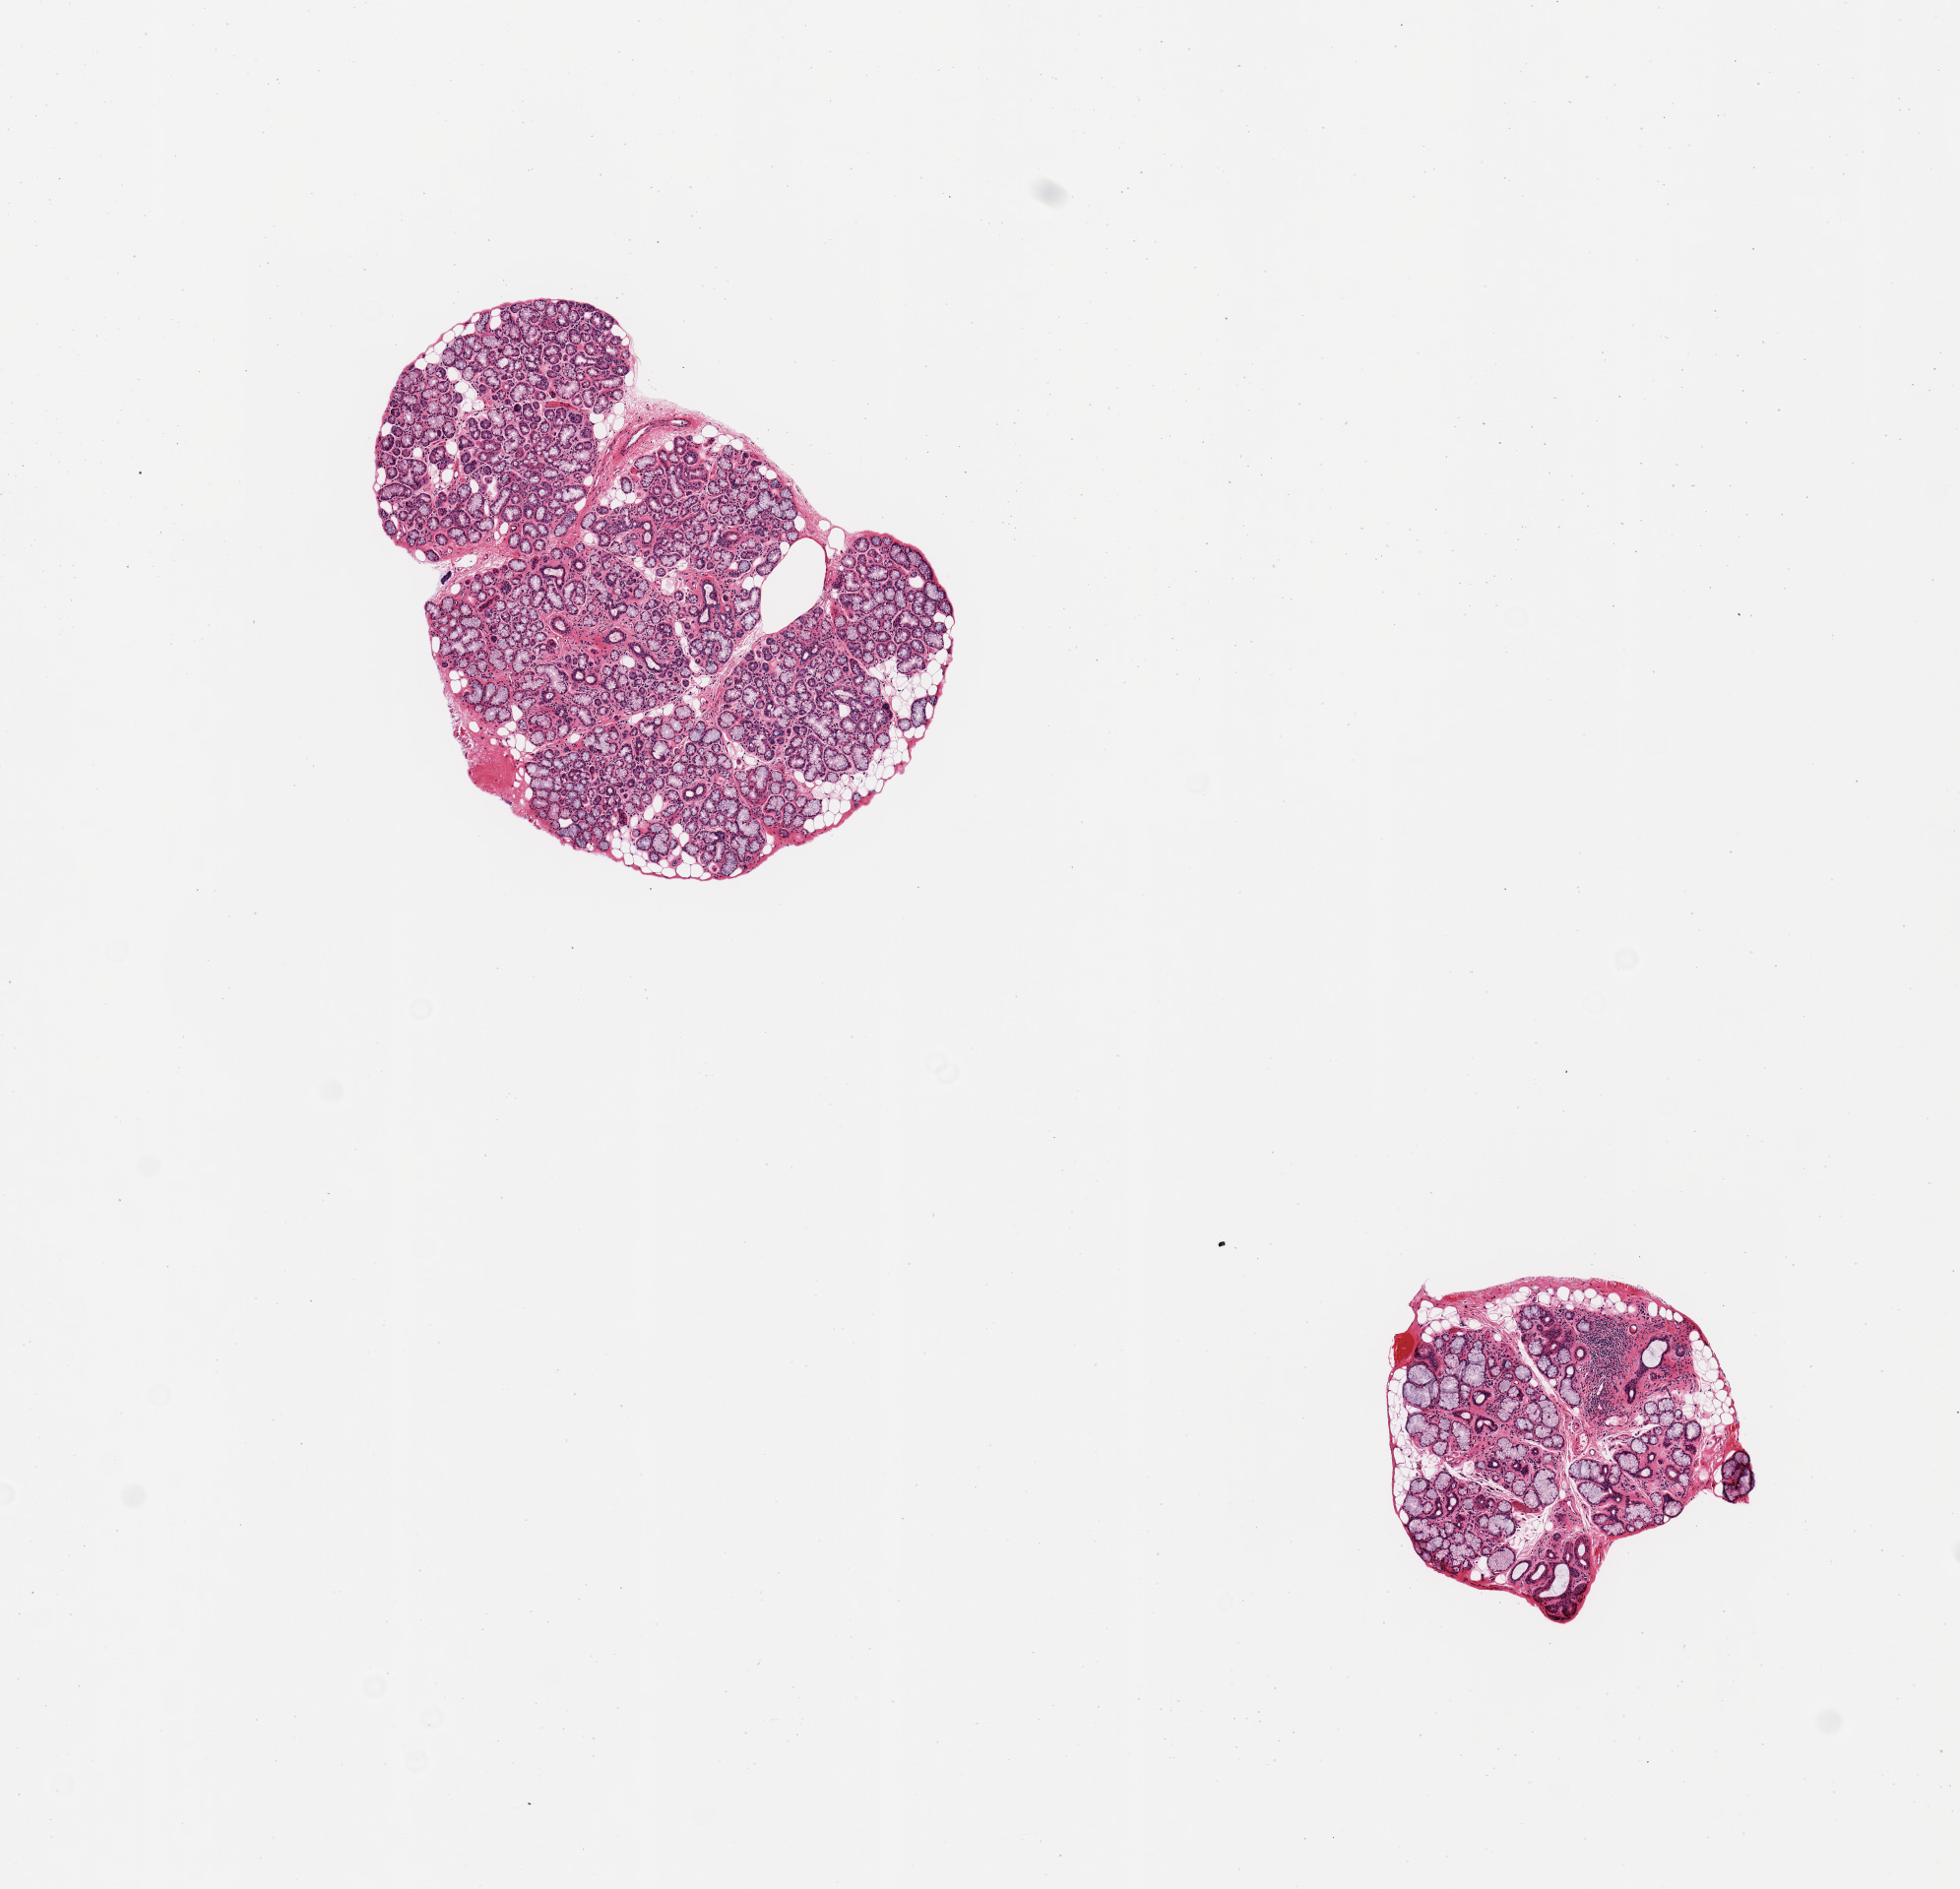
Digitized haematoxylin and eosin-stained section — shown as a low-resolution overview of the whole scanned area (about 7.9 x 7.6 mm, acquisition: 20x scan). PAXgene-fixed, paraffin-embedded tissue. Sampled site (target tissue): minor salivary gland. Tissue donor sample. Donor: male.
Reviewer comment on this tissue sample: 2 pieces, >90% target glandular tissue.